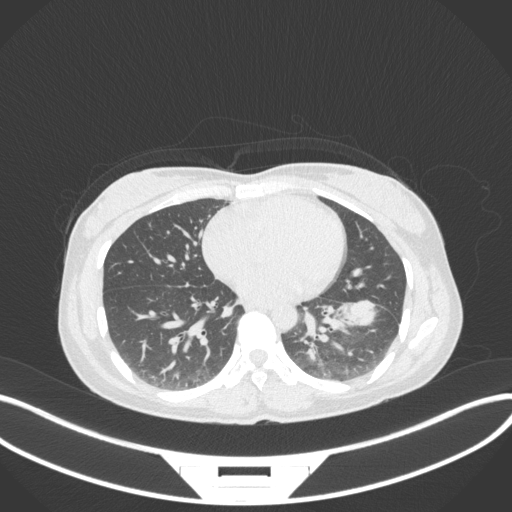
Chest CT, one axial slice; position 149 of 361 along the scan axis; reconstruction kernel B31f; lung window (W 1500 / L -600 HU); 512 × 512 image matrix, field of view 400 × 400 mm. Patient: female, 41 years. Case-level facts recorded for this patient, not image findings: clinical TNM (as recorded): T2a N3 M1b.
Outlined on this slice (bounding box drawn by a radiologist):
- lung tumour (recorded histology: adenocarcinoma): bounding box <330,292,385,331> (left, top, right, bottom; pixels)